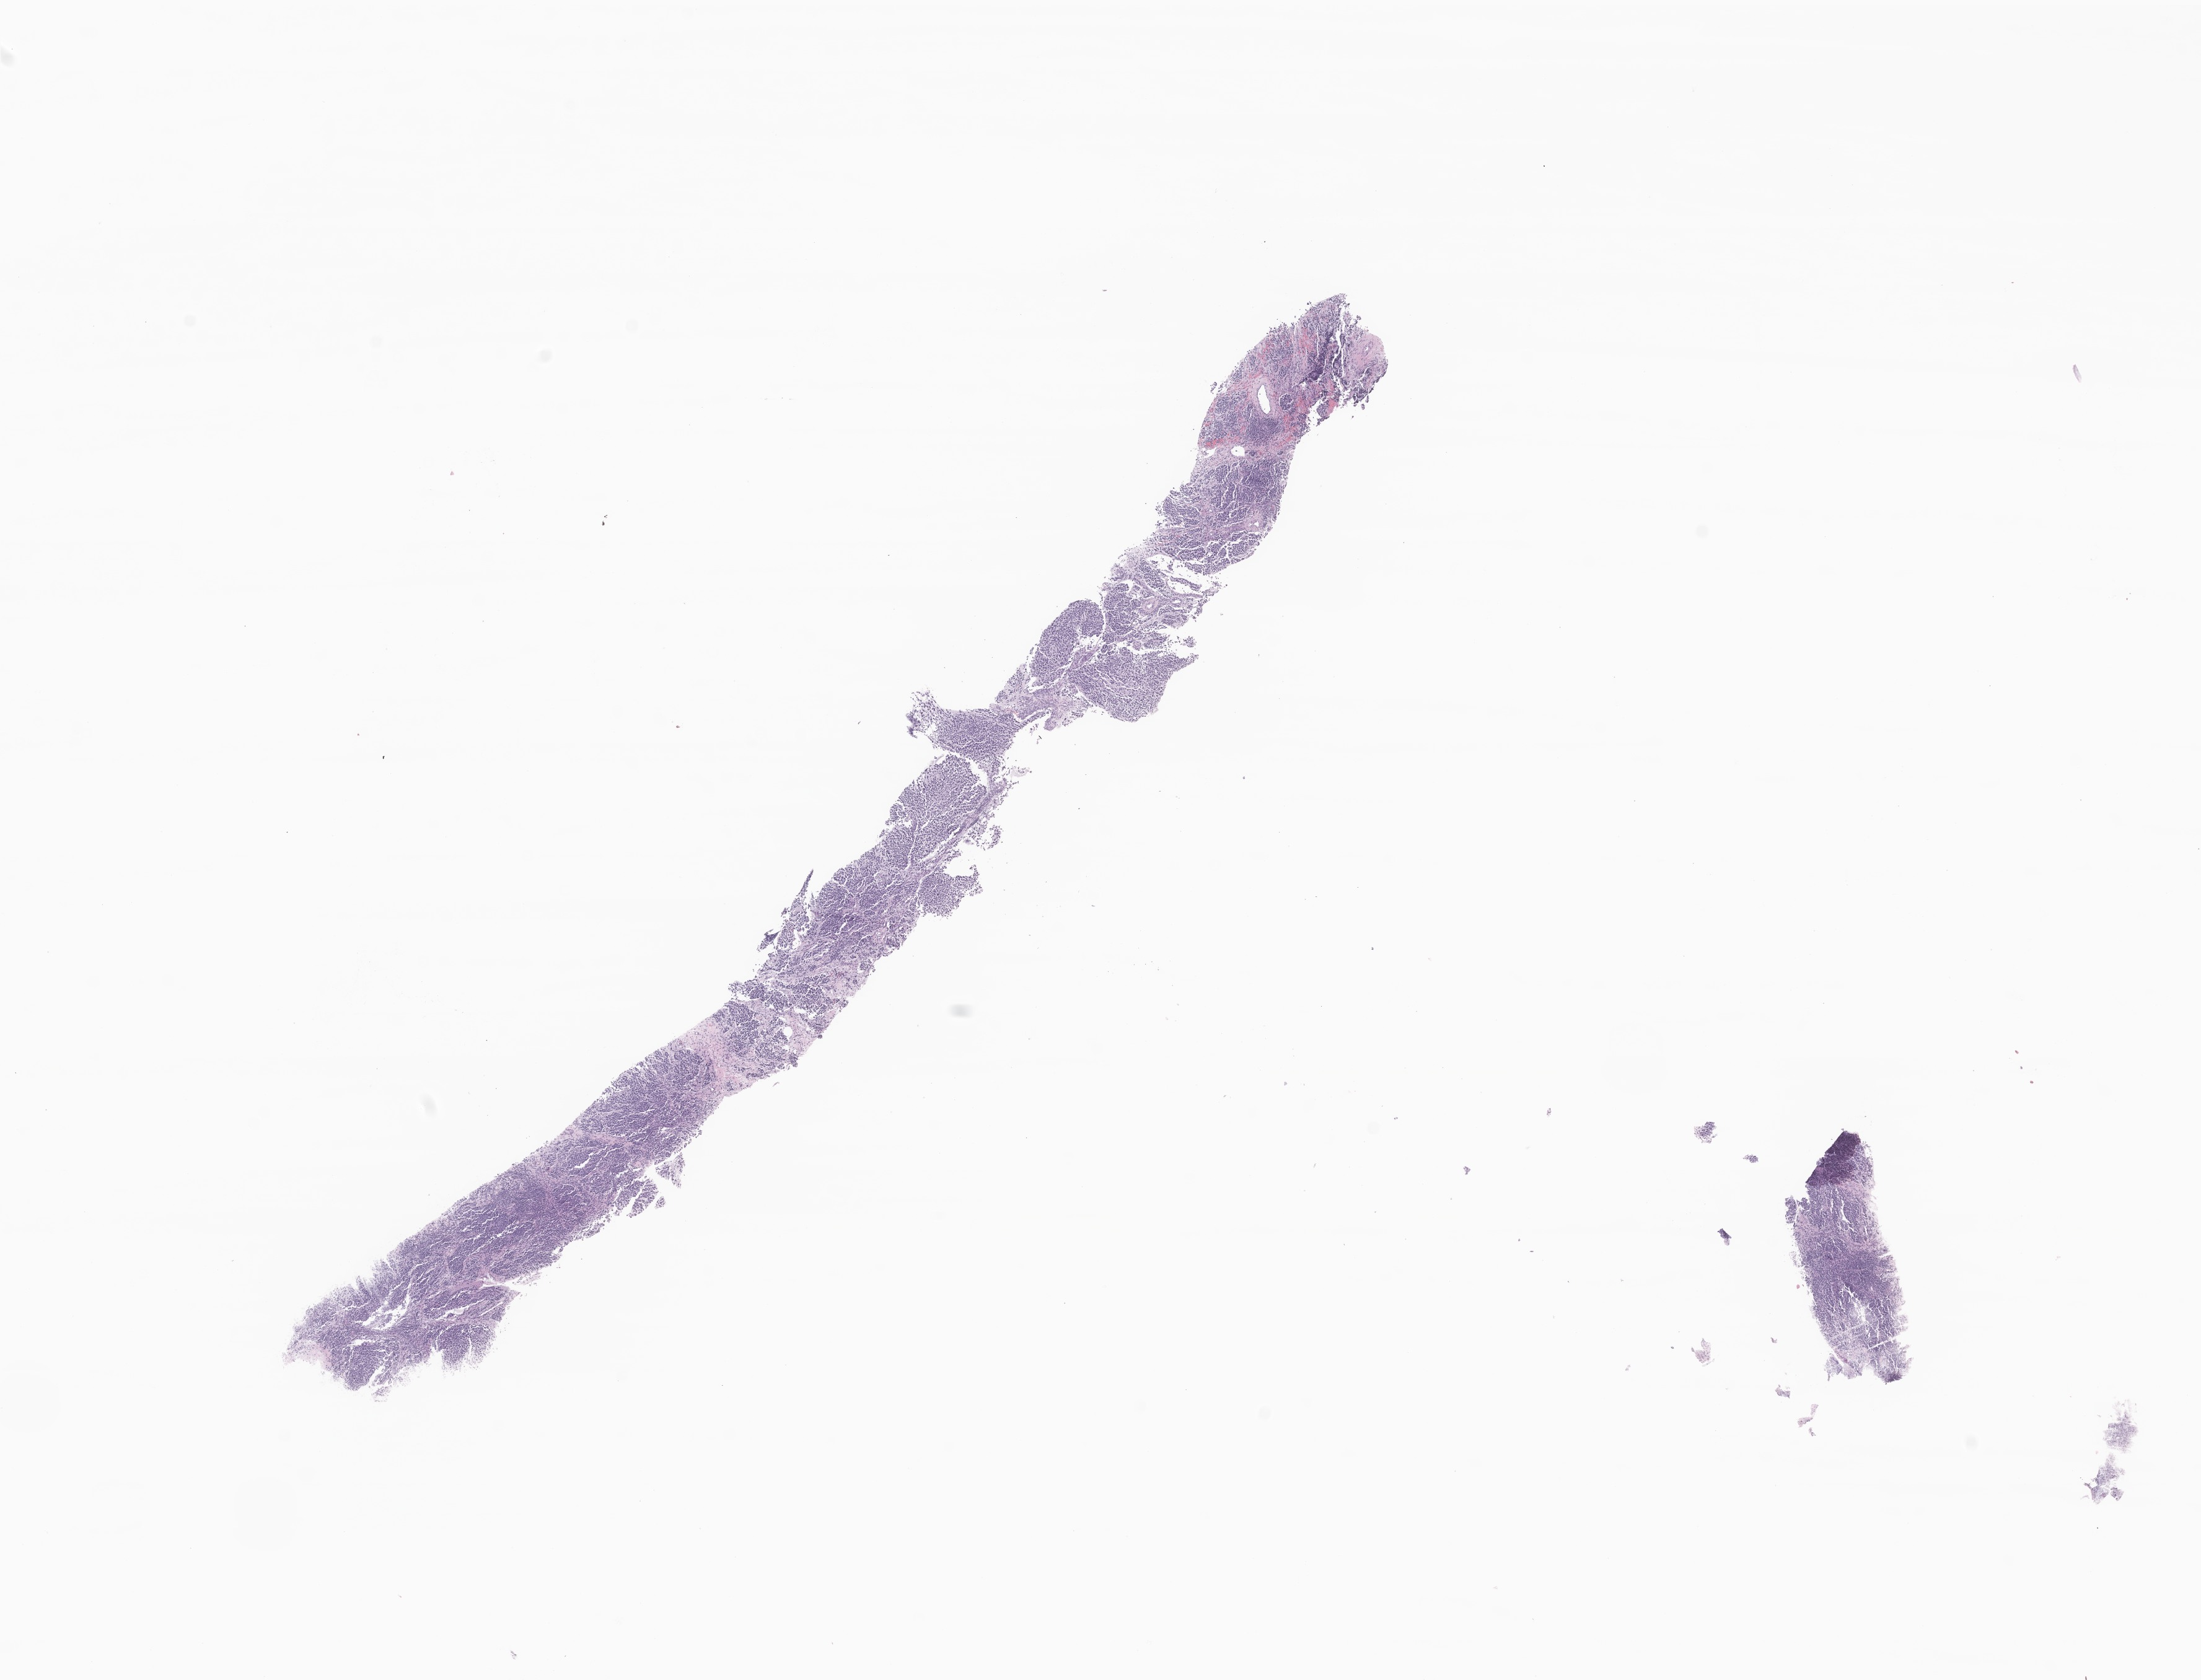
Hematoxylin and eosin (H&E) whole-slide image of tumor tissue from the abdomen — a low-resolution overview of the entire scanned area, about 15.0 x 11.4 mm. Formalin-fixed paraffin-embedded section. Patient: female, age 345 days.
* recorded diagnosis: Neuroblastoma, NOS